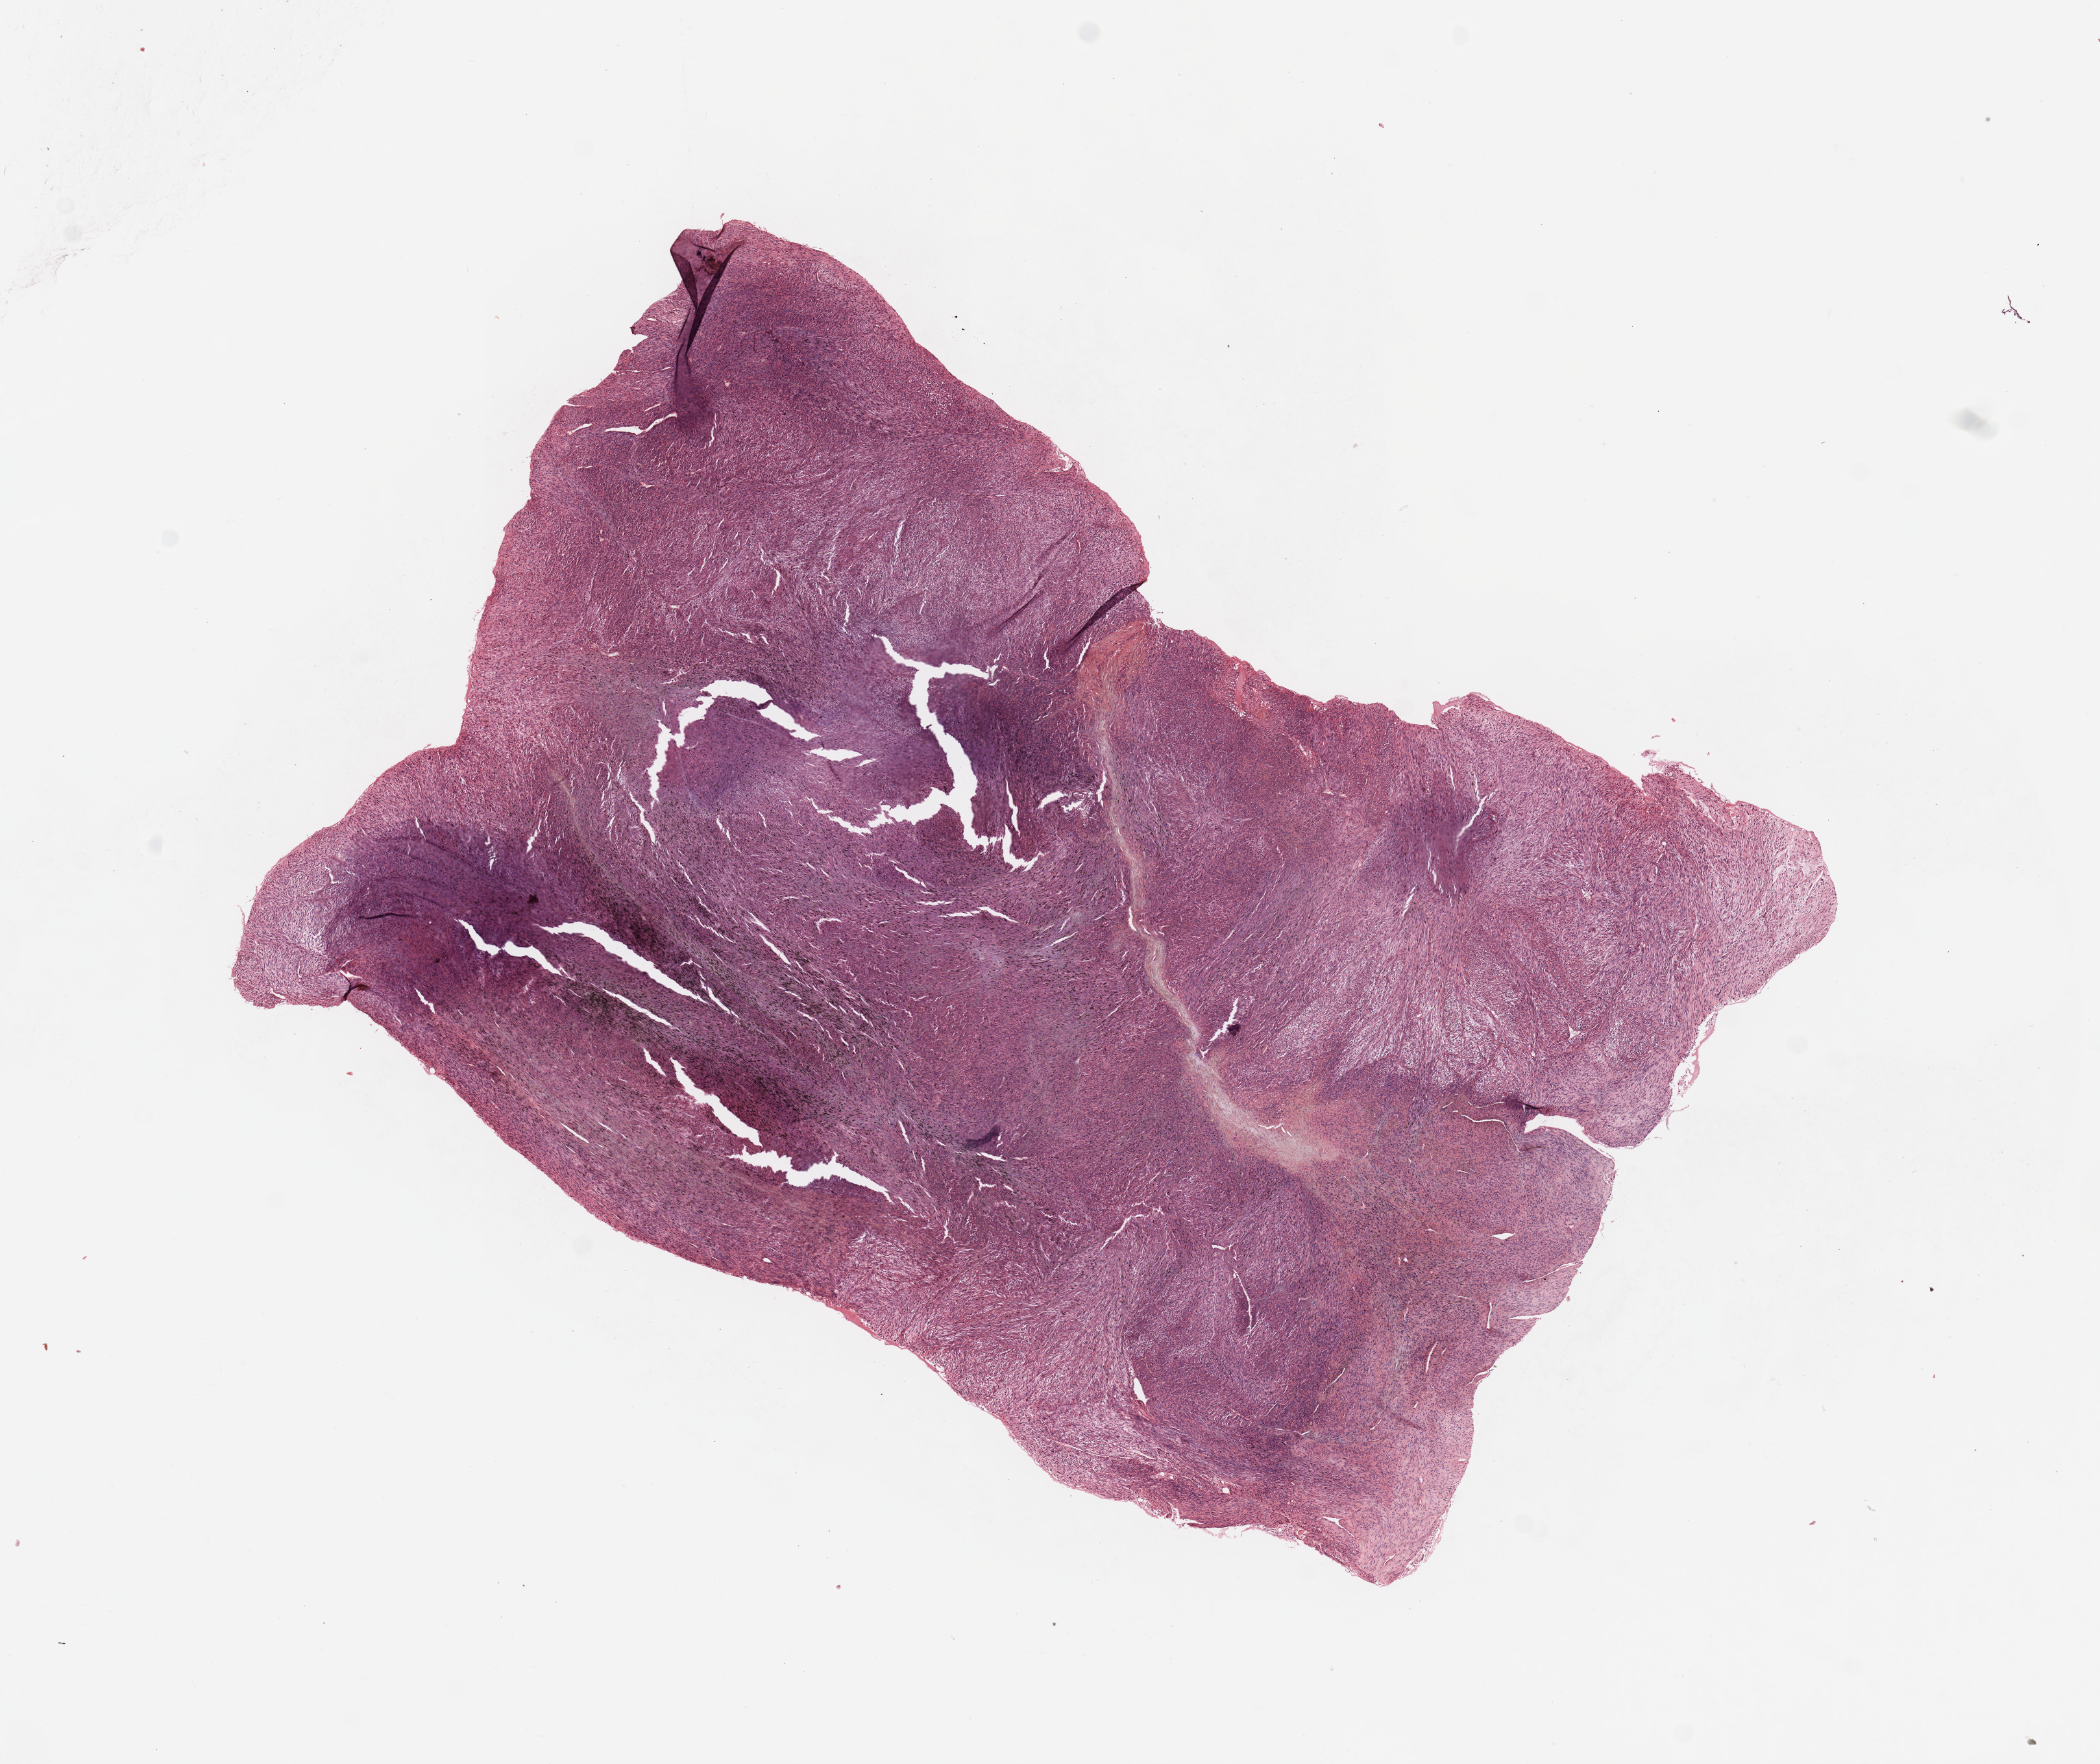
Whole-slide histology image, H&E-stained, shown as a low-resolution overview of the whole scanned area (about 12.8 x 10.7 mm, from a 20x scan), tumour tissue sample. Male, 66 y/o.
* primary tumour site (as recorded): chest
* patient diagnosis (cohort enrolment): sarcoma (site not recorded at cohort level)